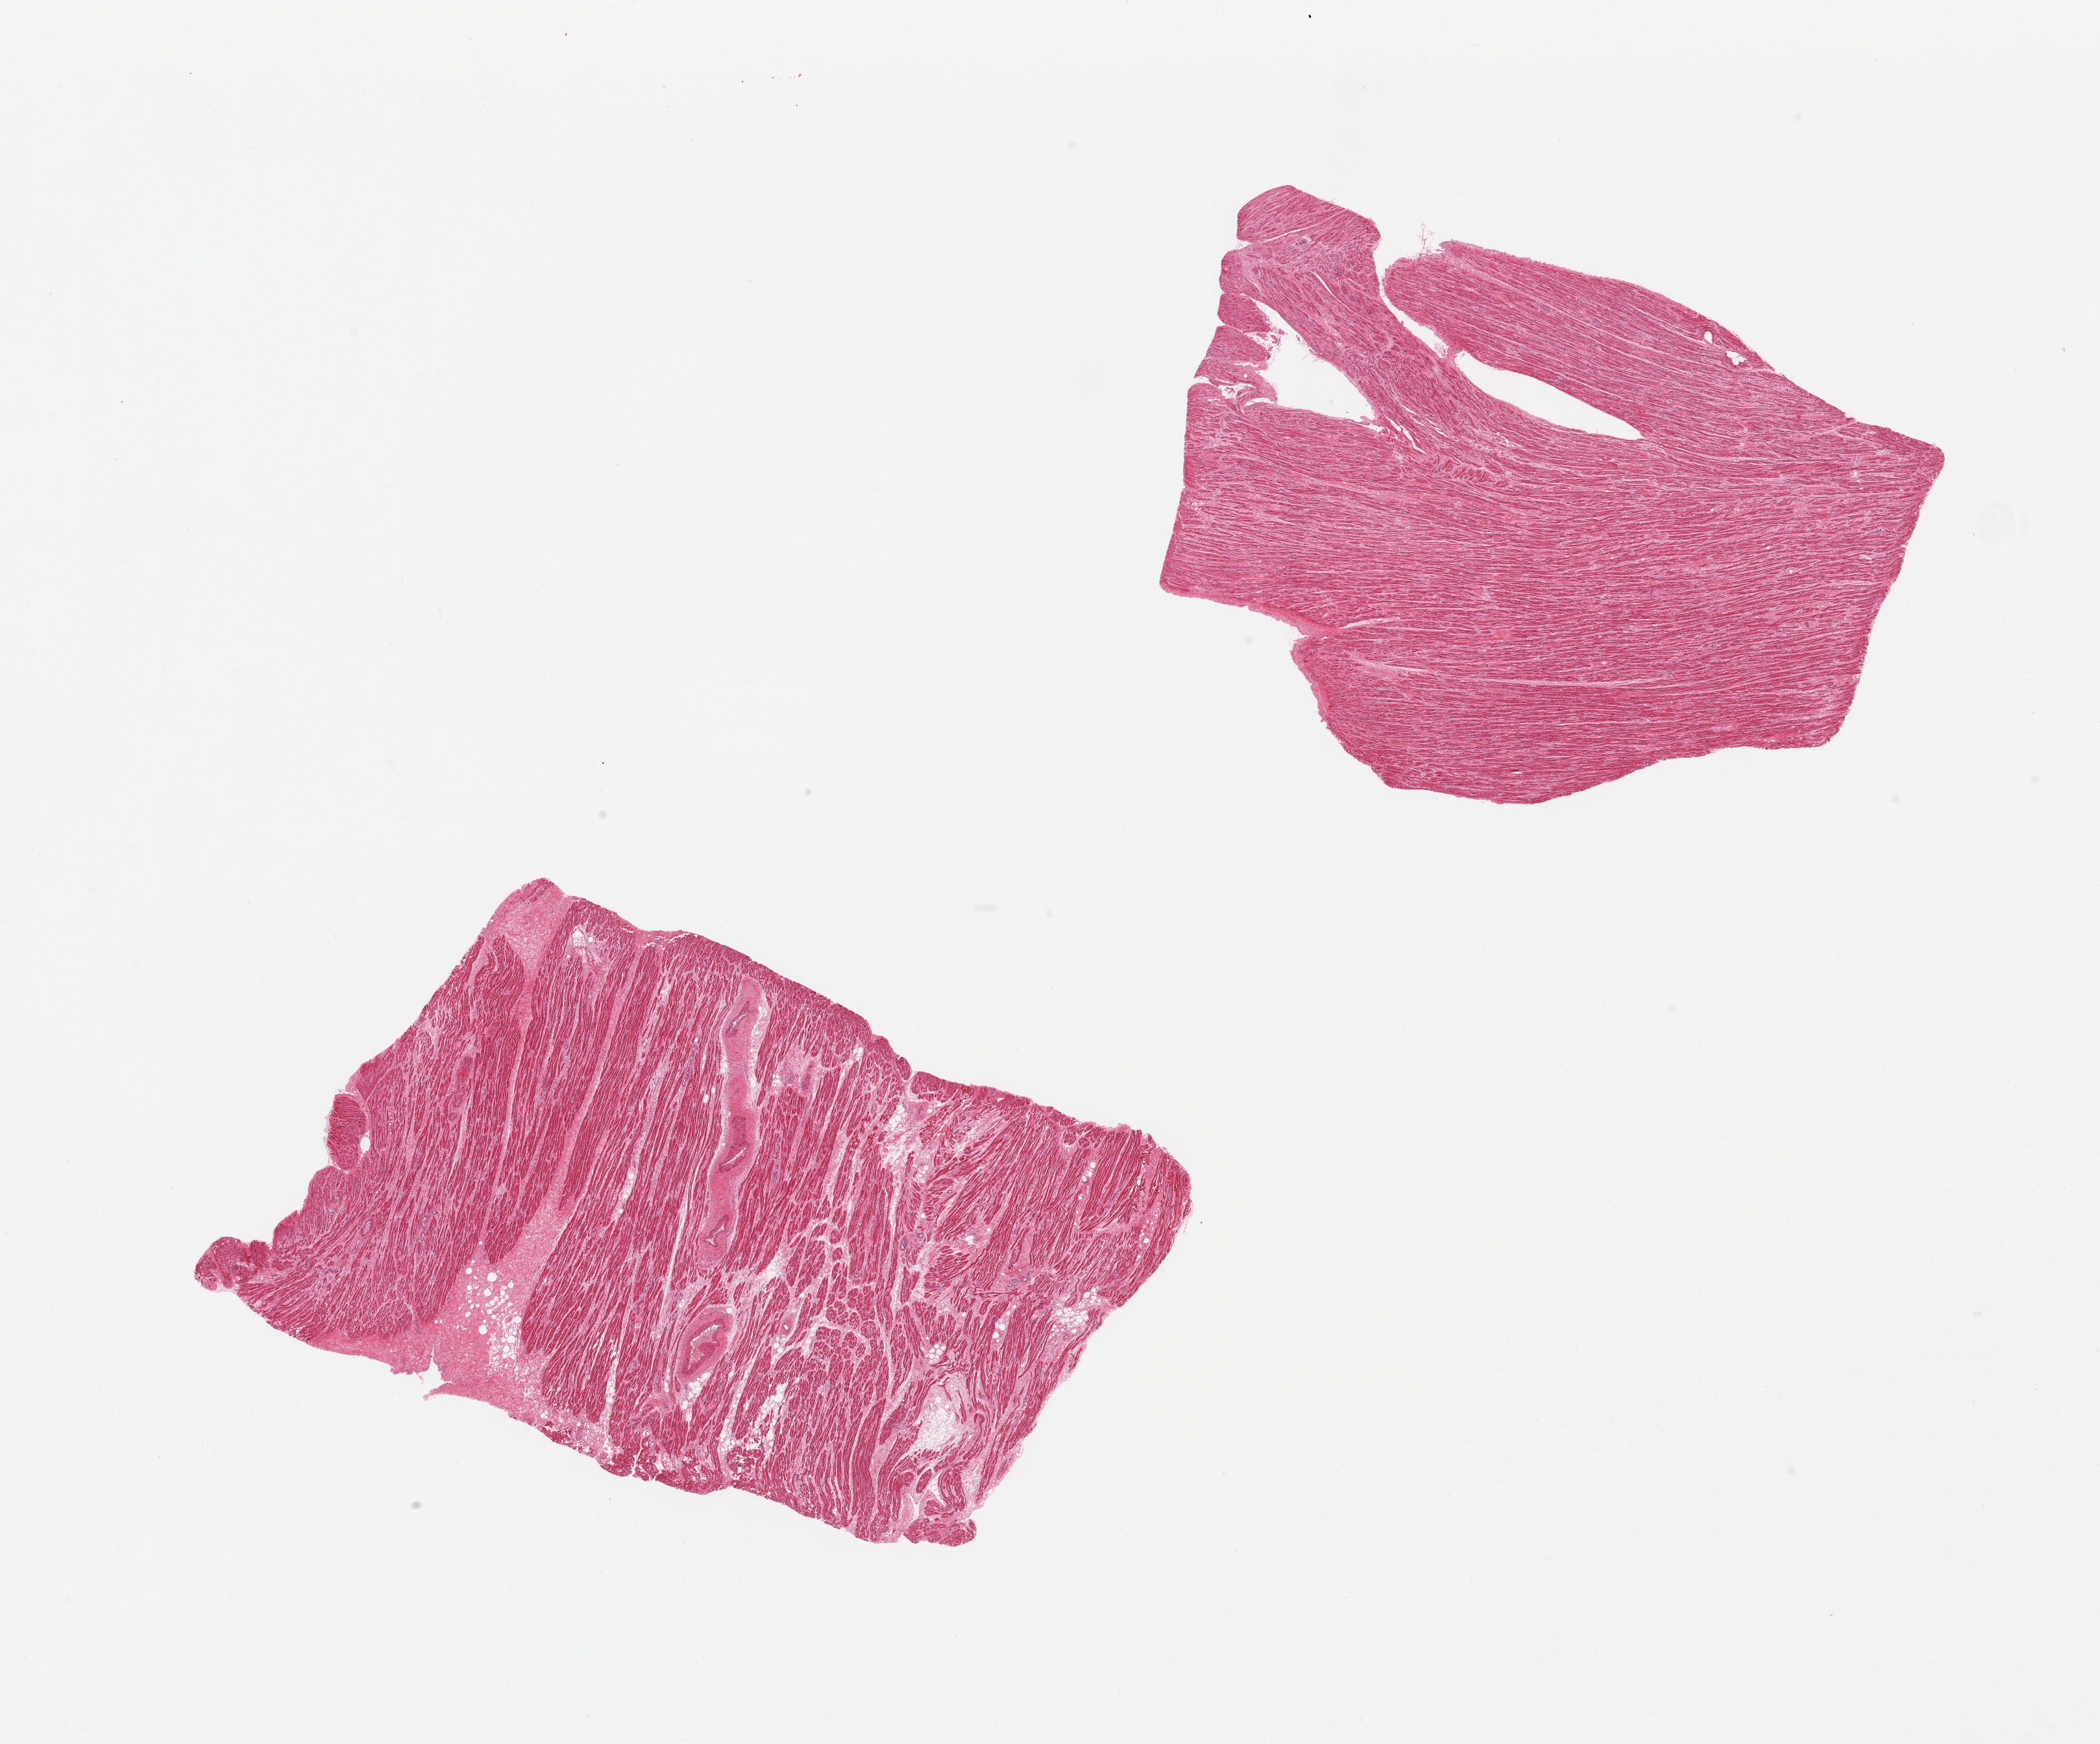
Digitized H&E-stained section — shown as a low-resolution overview of the whole scanned area (about 25.6 x 21.3 mm, acquisition: 20x scan); PAXgene-fixed, paraffin-embedded tissue; sampled site (target tissue): auricular appendage; tissue donor sample. Donor sex: male.
Reviewer comment on this tissue sample: 2 pieces, no abnormalities.